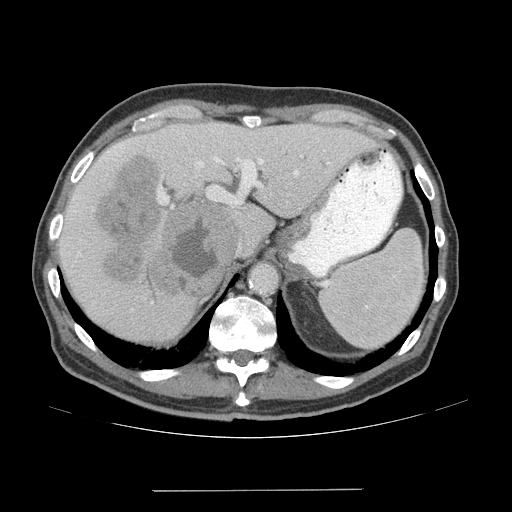
Contrast-enhanced abdominal CT (liver protocol), one axial slice; position 47 of 77 along the scan axis; reconstruction kernel STANDARD; 140 kVp; soft-tissue window (W 400 / L 40 HU); 2.5 mm slice thickness; 512 × 512 image matrix, field of view 400 × 400 mm. From the clinical record (not read from this slice): diagnosis: hepatocellular carcinoma (patient treated with transarterial chemoembolisation; whether this scan precedes or follows treatment is not stated here); TNM stage (as recorded): Stage-IVA; Child-Pugh class: A; tumour differentiation: well differentiated; tumour nodularity: uninodular.
Outlined on this slice (semi-automatic segmentation, software-assisted and operator-edited):
- liver parenchyma outside the tumour (the mass and vessels are separate outlines, so this box may not span the whole liver): bounding box [x1, y1, x2, y2] px = [58, 122, 374, 341]
- mass: [97, 156, 239, 297]
- liver vessels: [74, 131, 330, 303]